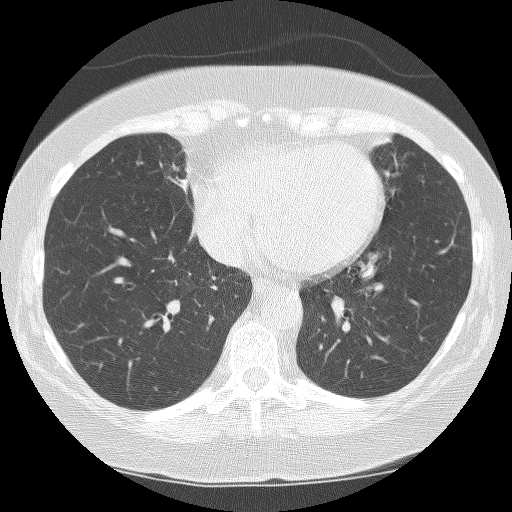
Low-dose screening chest CT, one axial slice. 120 kVp. Lung window (W 1500 / L -600 HU). 512 × 512 image matrix, field of view 299 × 299 mm.
Annotated regions visible in this slice (manually delineated by an expert):
- lesion 1 (tumor, hilum of right lung): box from (x=170, y=162) to (x=190, y=196) px